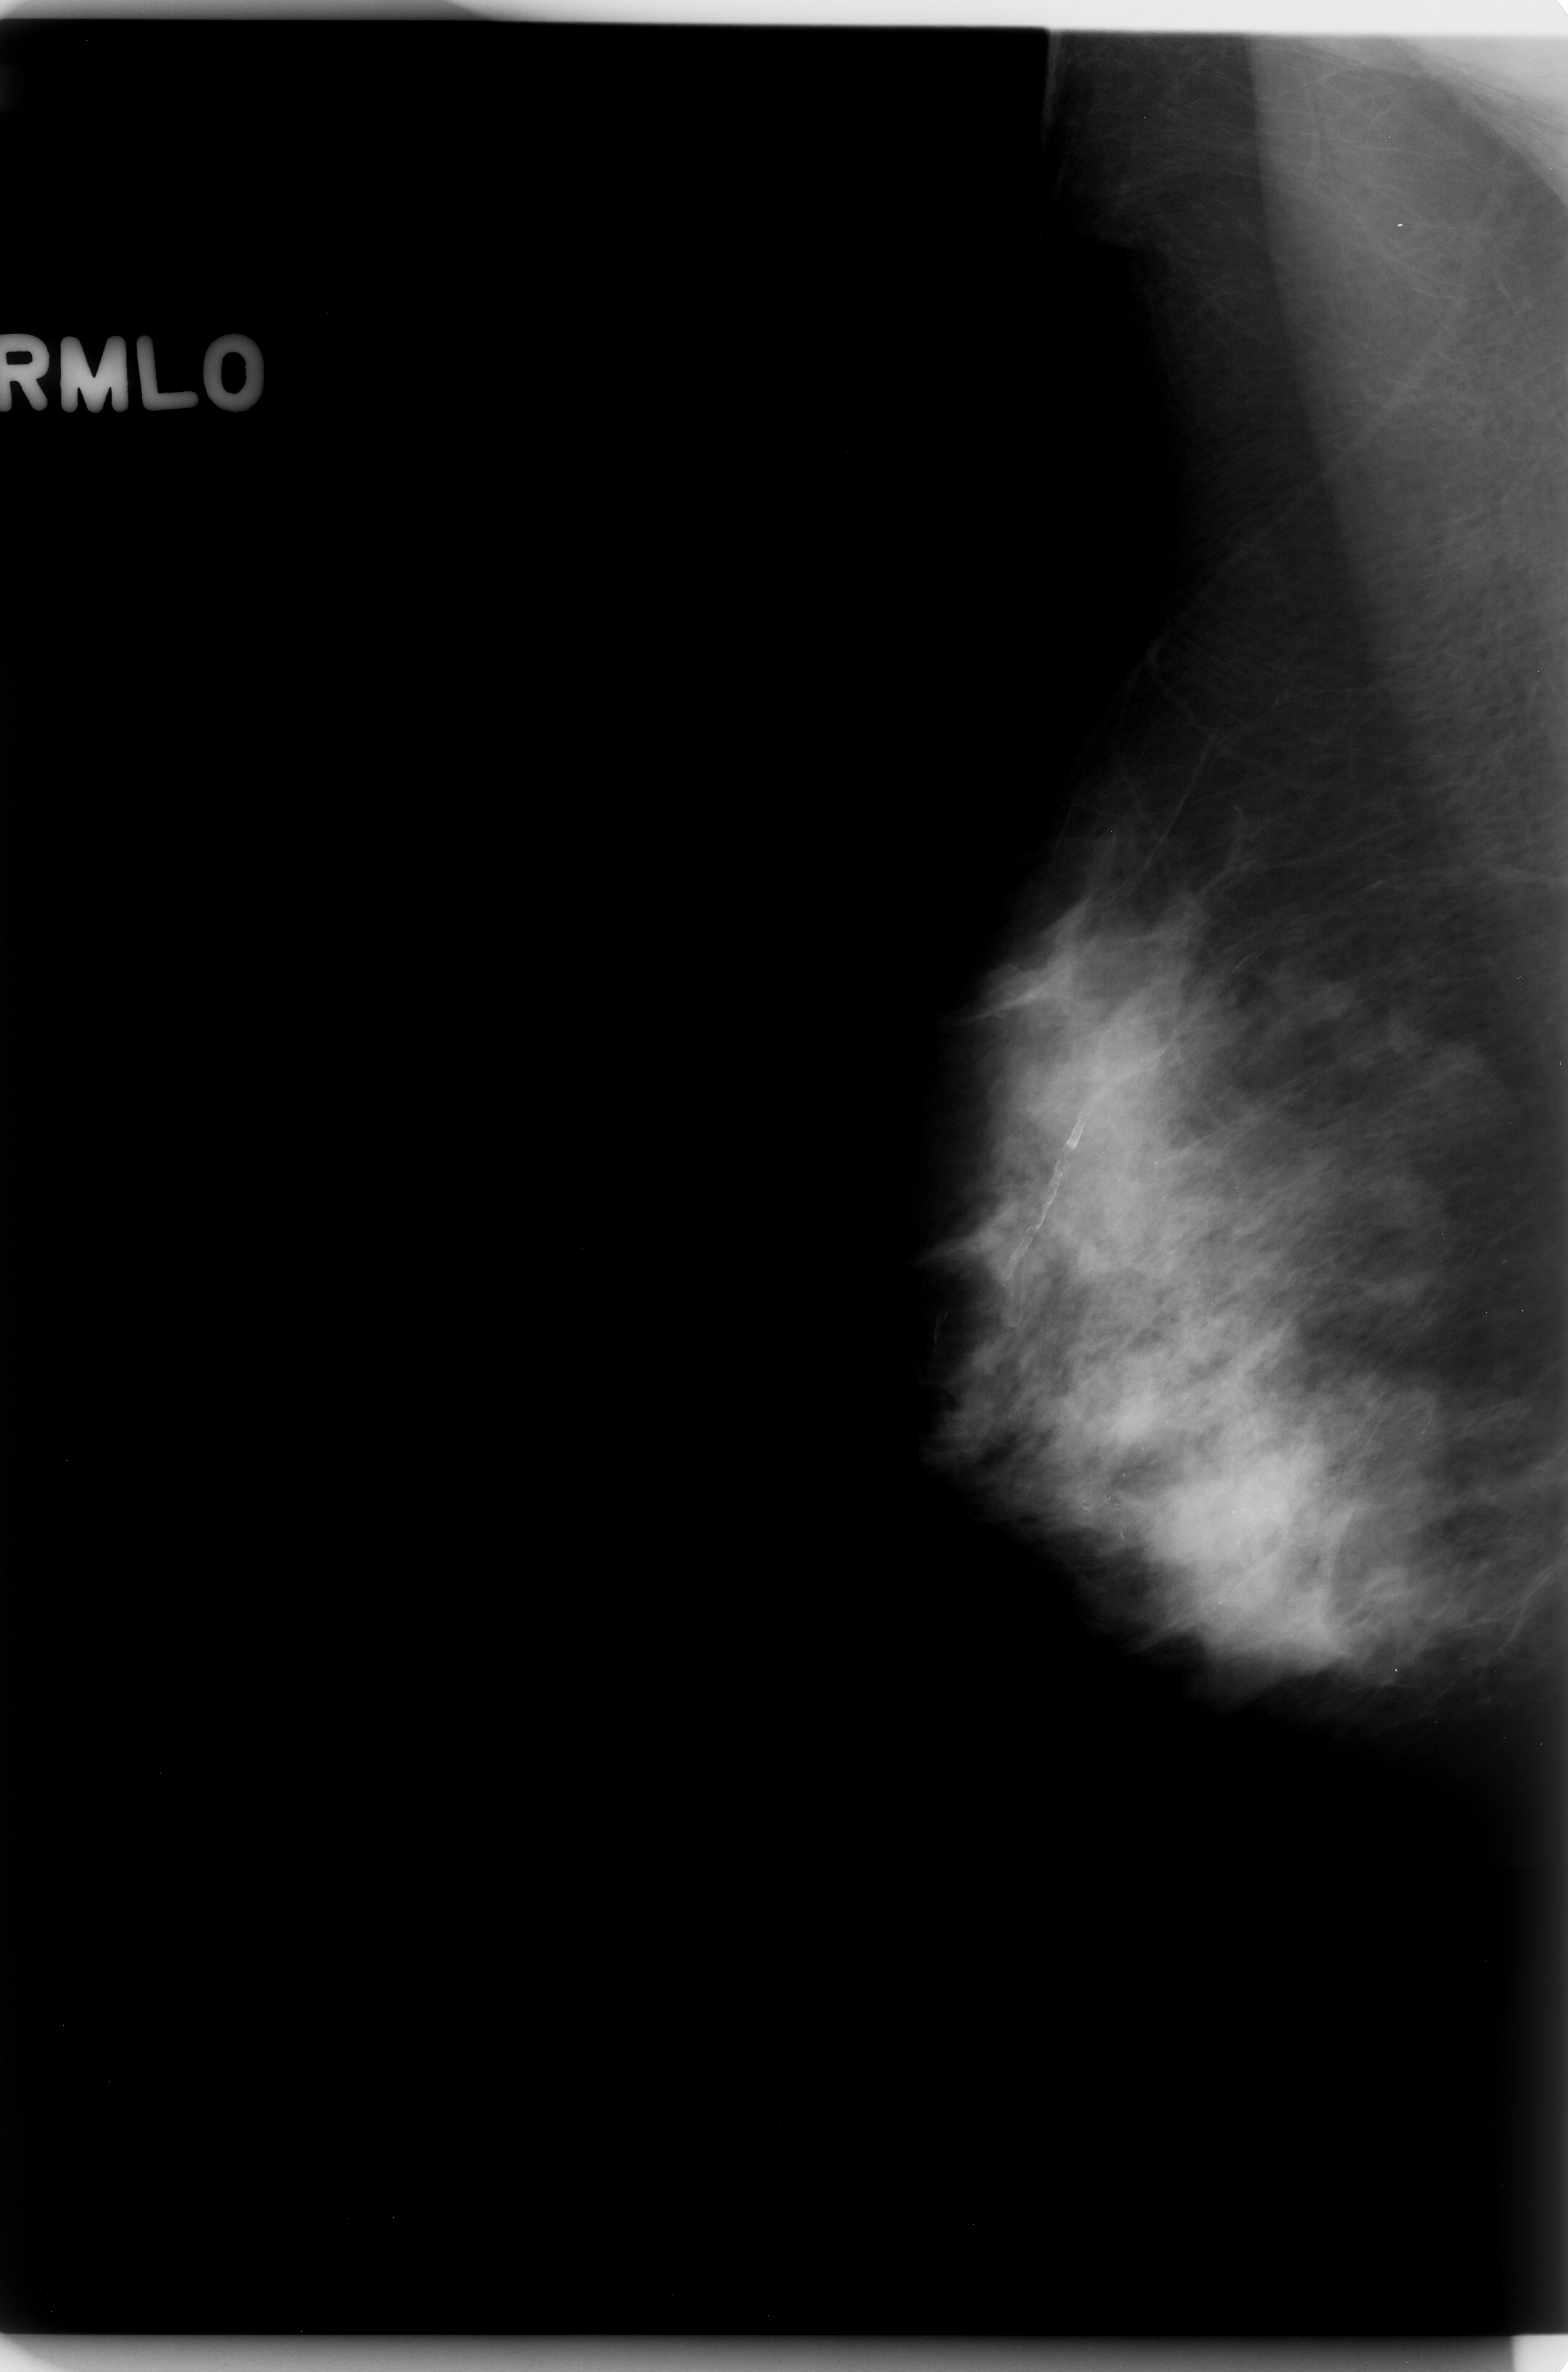
Digitized screen-film mammogram; right breast; mediolateral oblique (MLO) view; 1568 × 2372 image matrix.
Expert-marked regions of interest on this image (one box per marked abnormality):
- calcifications, morphology fine linear branching, distribution segmental; BI-RADS assessment category 5; pathology result (as recorded, not read from the image): malignant: box from (x=1034, y=1410) to (x=1370, y=1576) px